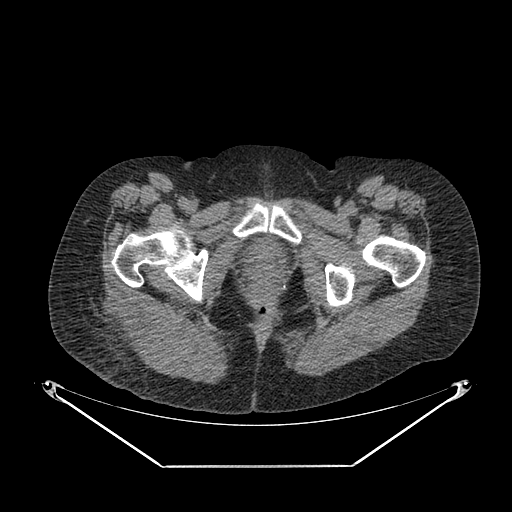
CT of an extremity soft-tissue mass (from a PET/CT study), one axial slice. Position 47 of 267 along the scan axis. Reconstruction kernel SOFT. Soft-tissue window (W 400 / L 40 HU). 512 × 512 image matrix, field of view 500 × 500 mm. Female patient. From the clinical record (not read from this slice): histological type: spindle cell suggestive of myxofibrosarcoma; grade: intermediate; site of the primary tumour: right buttock.
Annotated regions visible in this slice (expert contour drawn on MRI and transferred to this co-registered scan by the dataset authors):
- gross tumour volume (mass): bounding box [x1, y1, x2, y2] px = [107, 299, 179, 357]